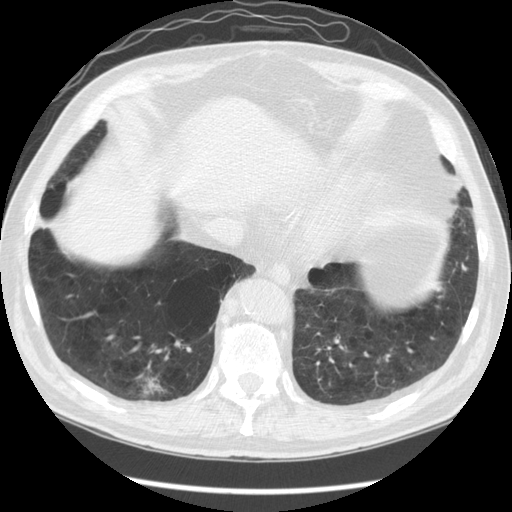
Chest CT (low-dose screening protocol), one axial image, baseline screening round, lung window (W 1500 / L -600 HU), slice 103 of 141 in the series, 512 × 512 image matrix. Male participant, aged 67 years at enrolment. Former smoker at enrolment.
Lesion marked by an expert reader, bounding box <121,355,184,411> (left, top, right, bottom; pixels). The screening reader recorded 2 non-calcified nodules or masses ≥4 mm on this exam (right lower lobe, right lower lobe); which of them this box marks is not recorded. Official screen result: positive, change unspecified: nodule(s) >= 4 mm or enlarging nodule(s), mass(es), or other non-specific abnormalities suspicious for lung cancer. Participant outcome: lung cancer diagnosed 78 days after this screen — squamous cell carcinoma, NOS, right lower lobe, moderately differentiated (G2), stage IA (AJCC 6th edition), 23 mm at pathology.